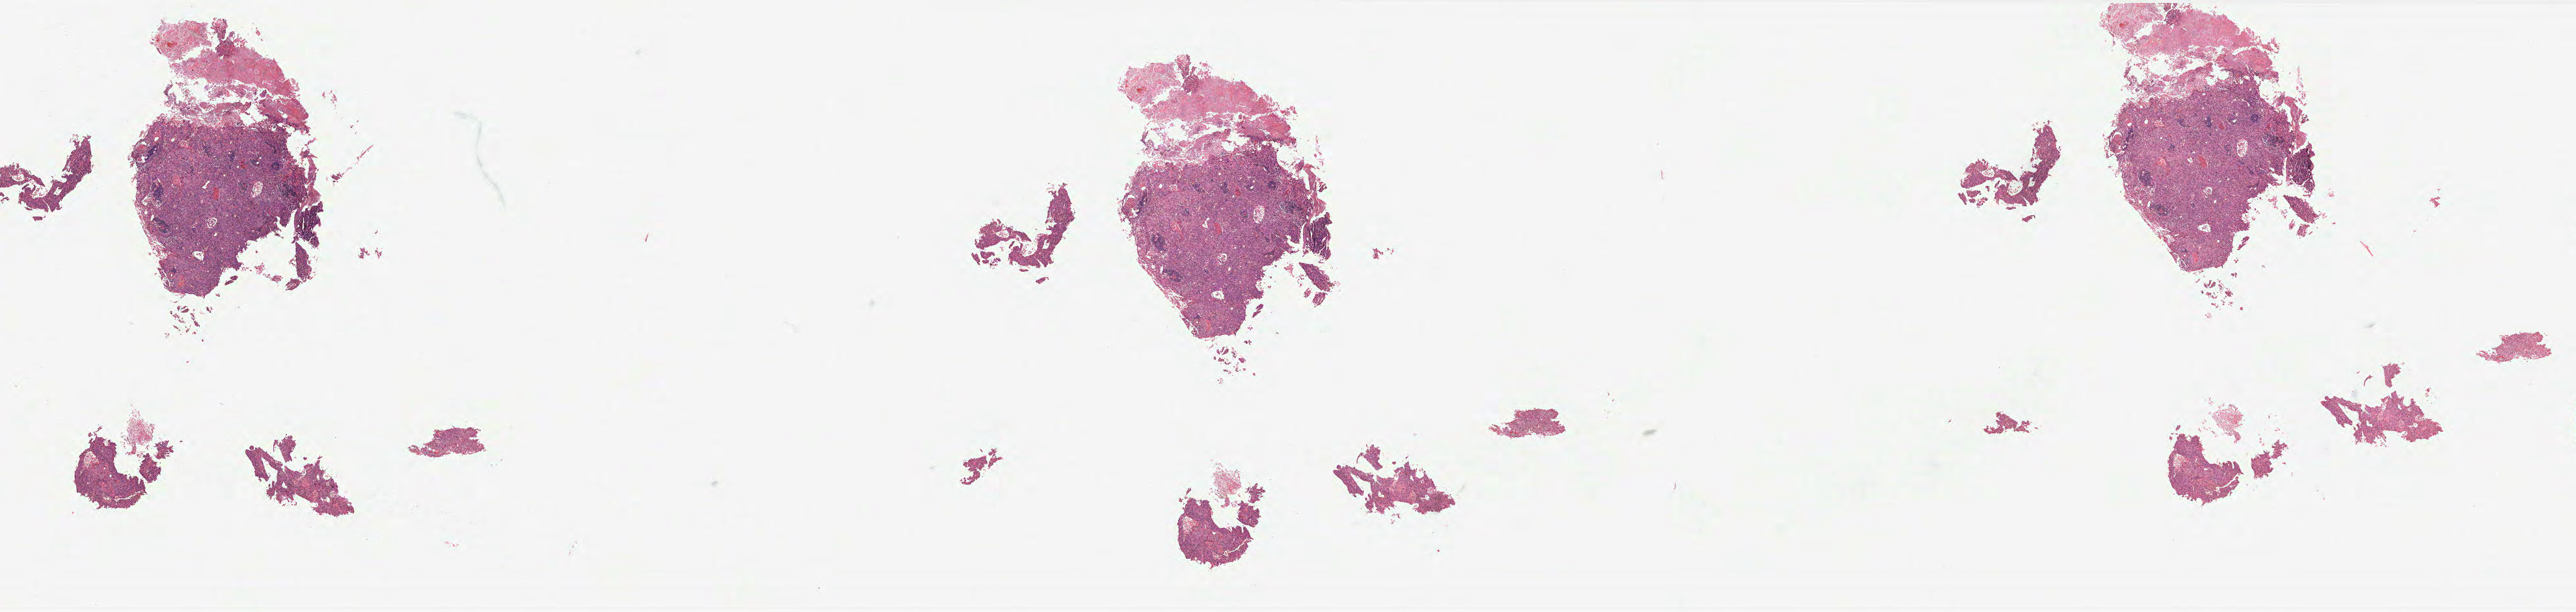
Whole-slide histology image, Hematoxylin and eosin (H&E) stained — whole scanned area (about 31.7 x 7.5 mm, acquisition: 40x scan) shown as a low-resolution overview, formalin-fixed paraffin-embedded (FFPE) diagnostic section, cervix, primary tumour sample. Female, age 39 years at initial diagnosis.
Histologic diagnosis: Squamous cell carcinoma, NOS. FIGO stage: IB1. Lymph nodes positive (case pathology): 0 of 33 examined.